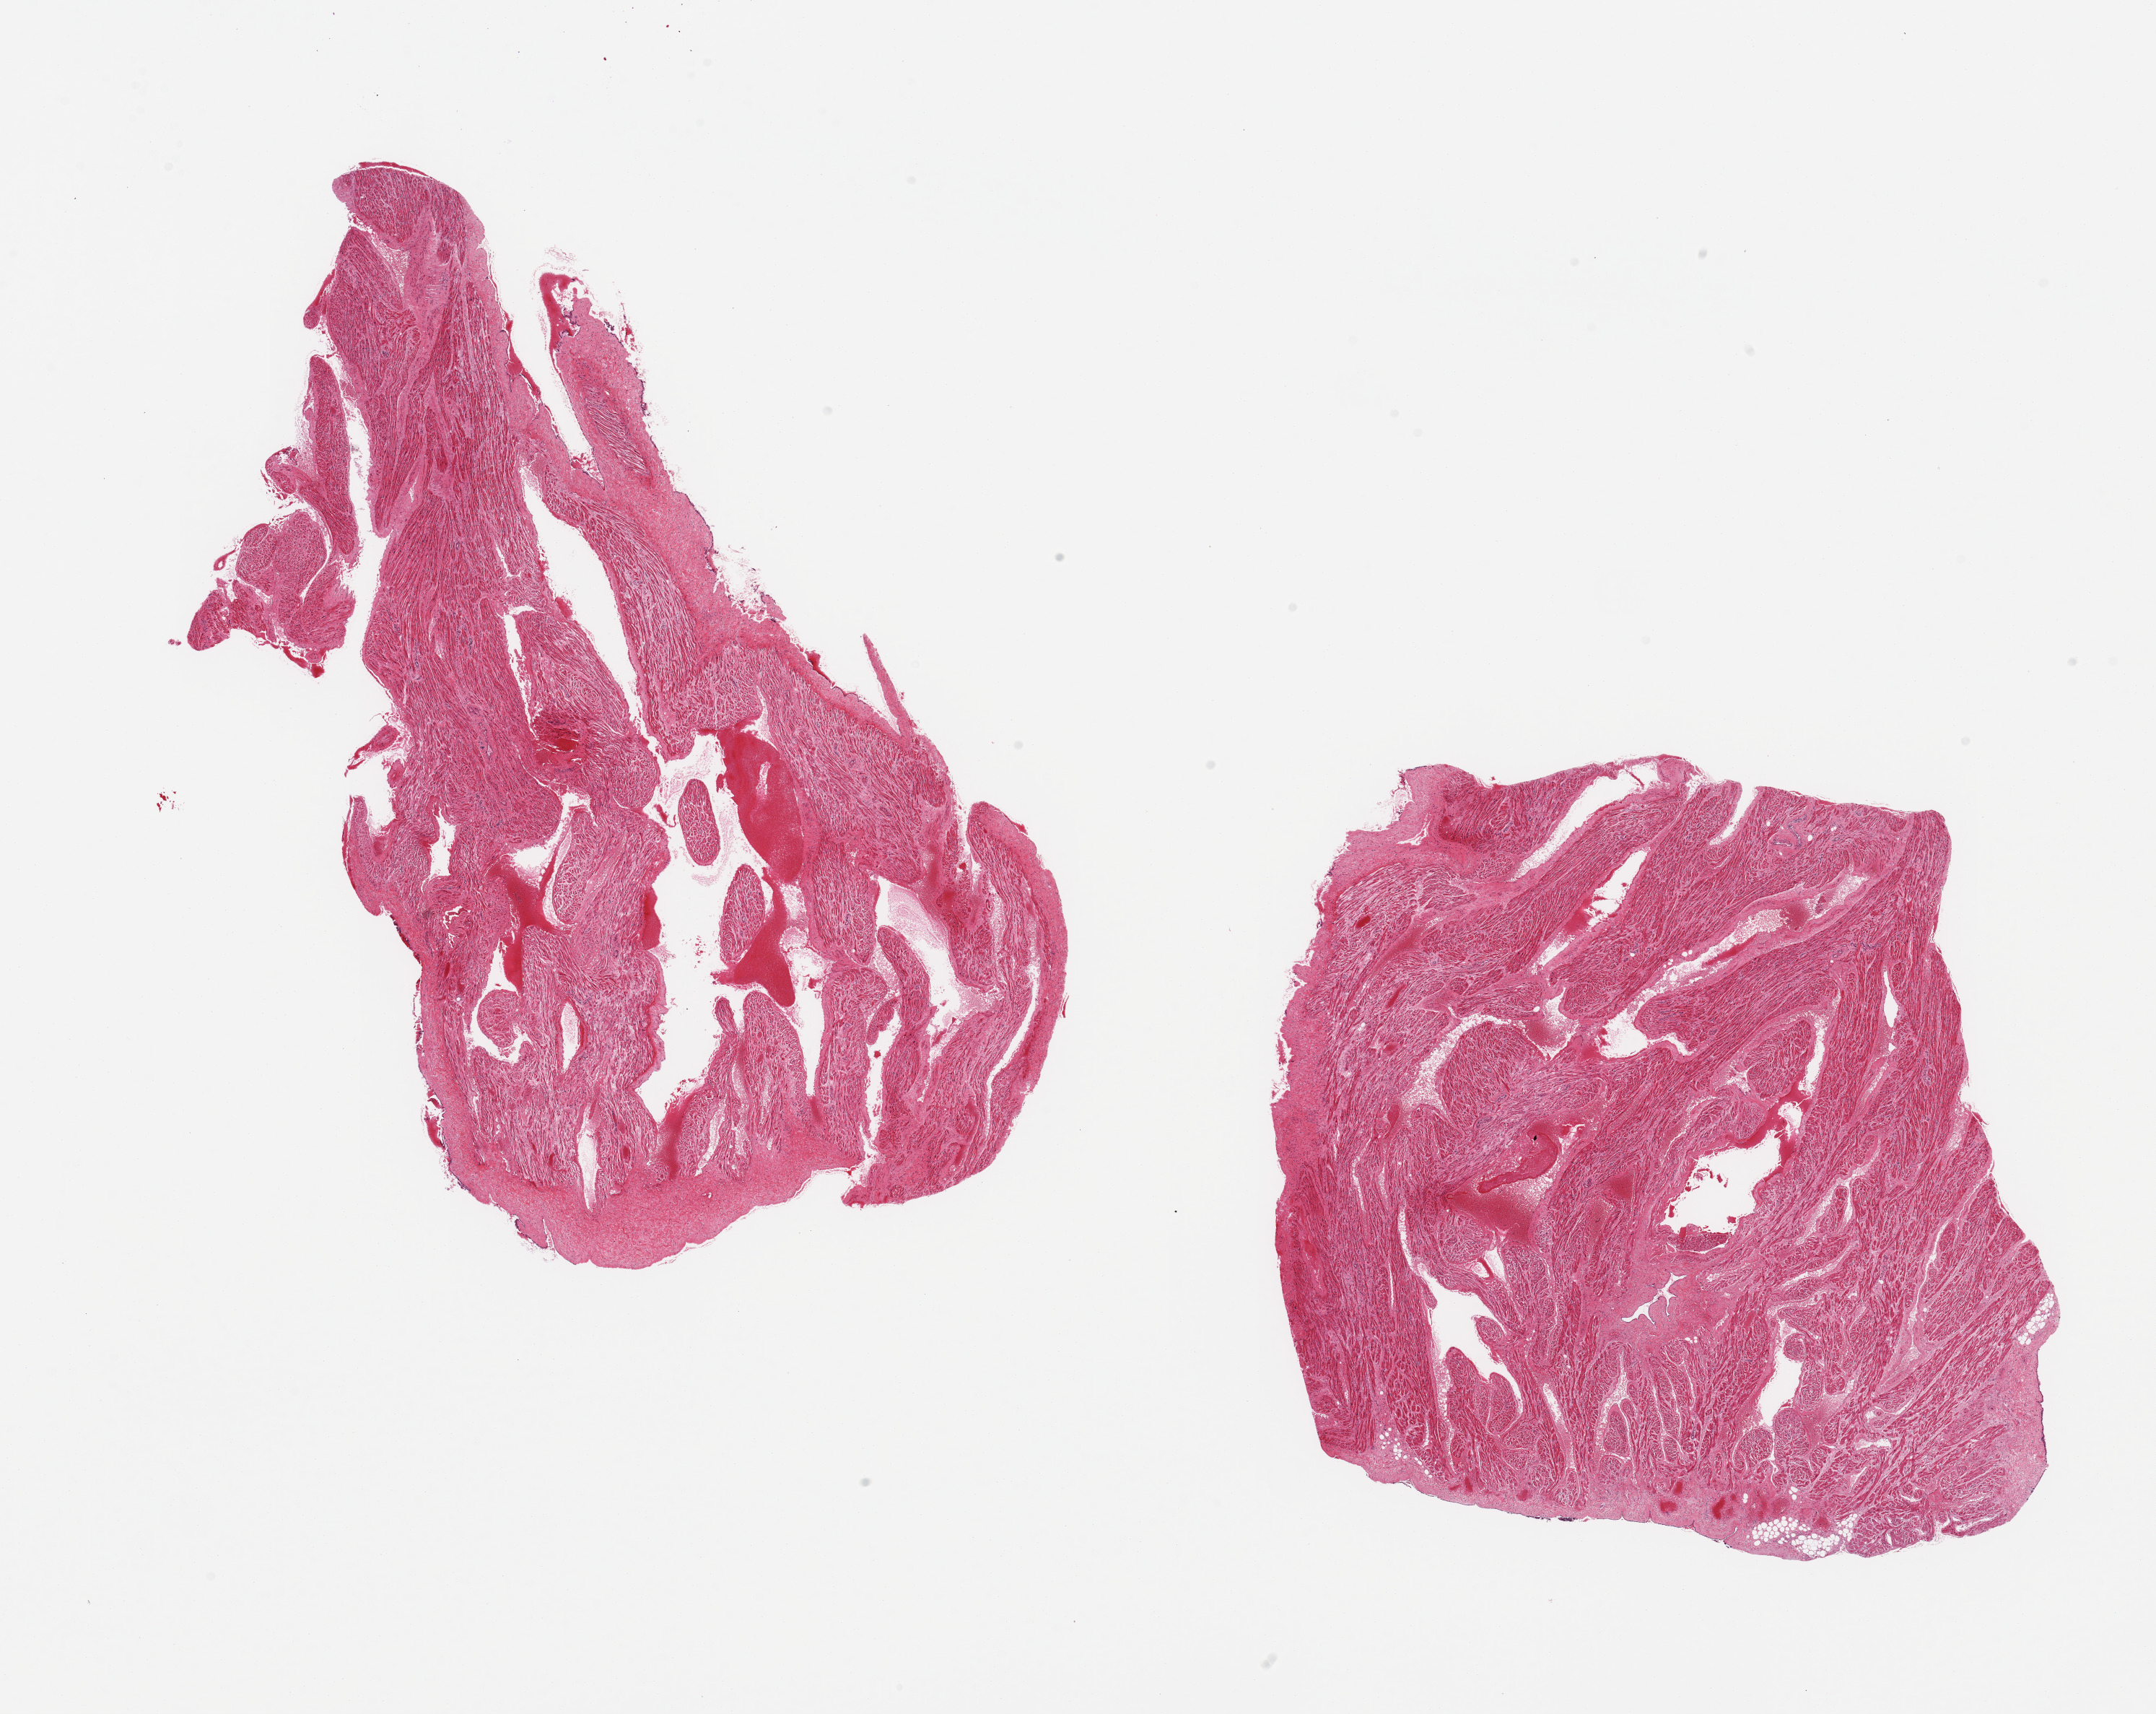
Digitized H&E-stained section, whole scanned area (about 23.6 x 18.8 mm, from a 20x scan) shown as a low-resolution overview. PAXgene-fixed, paraffin-embedded tissue. Target tissue: auricular appendage. Tissue donor sample.
Reviewer comment on this tissue sample: 2 pieces.